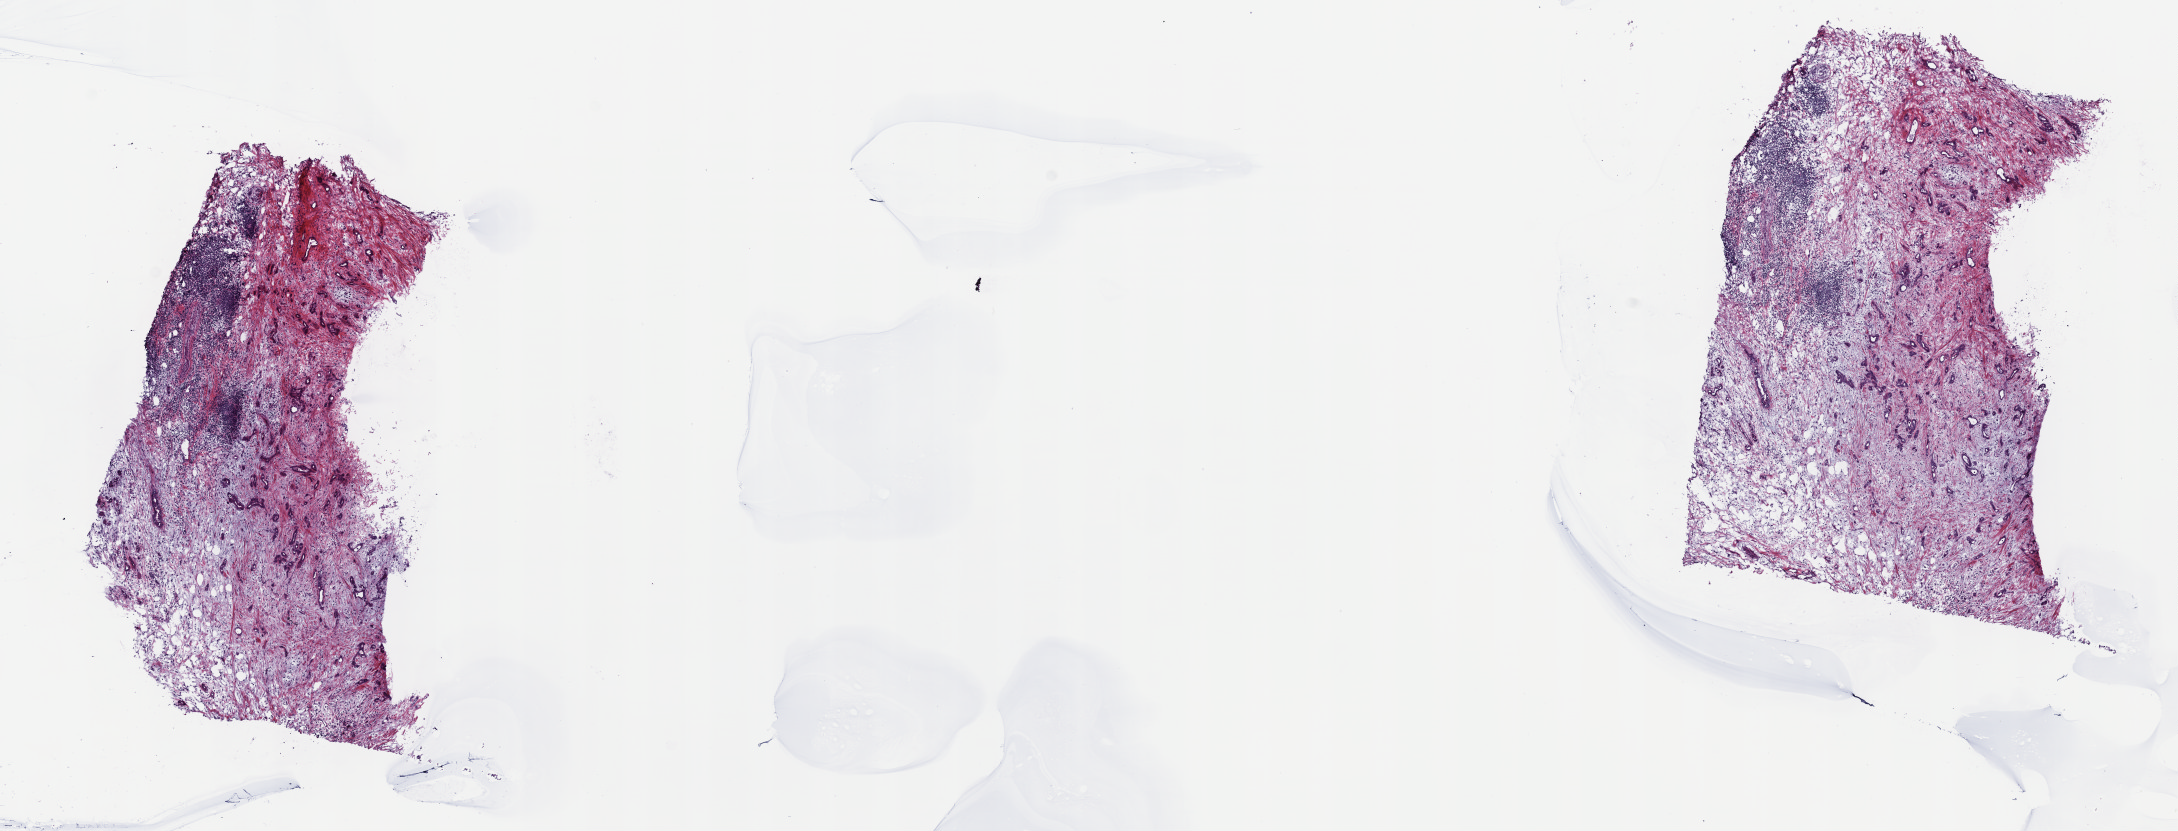
Hematoxylin and eosin (H&E) stained whole-slide image — low-resolution overview of the scanned area, about 17.6 x 6.7 mm (acquisition: 40x scan); frozen section from the top of the tissue portion; pancreas, primary tumour sample. Male patient; age at initial diagnosis 40 years. Histologic grade: G2 (moderately differentiated). Composition of this section per pathologist review: tumour cells 65%, tumour nuclei 25%, normal cells 35%, stromal cells 0%, necrosis 0%. Inflammatory infiltration, as recorded: lymphocyte infiltration 0%, monocyte infiltration 0%, neutrophil infiltration 0%.
Pathologic diagnosis: Infiltrating duct carcinoma, NOS. AJCC pathologic stage: IA (7th edition). TNM: T1 N0 MX.